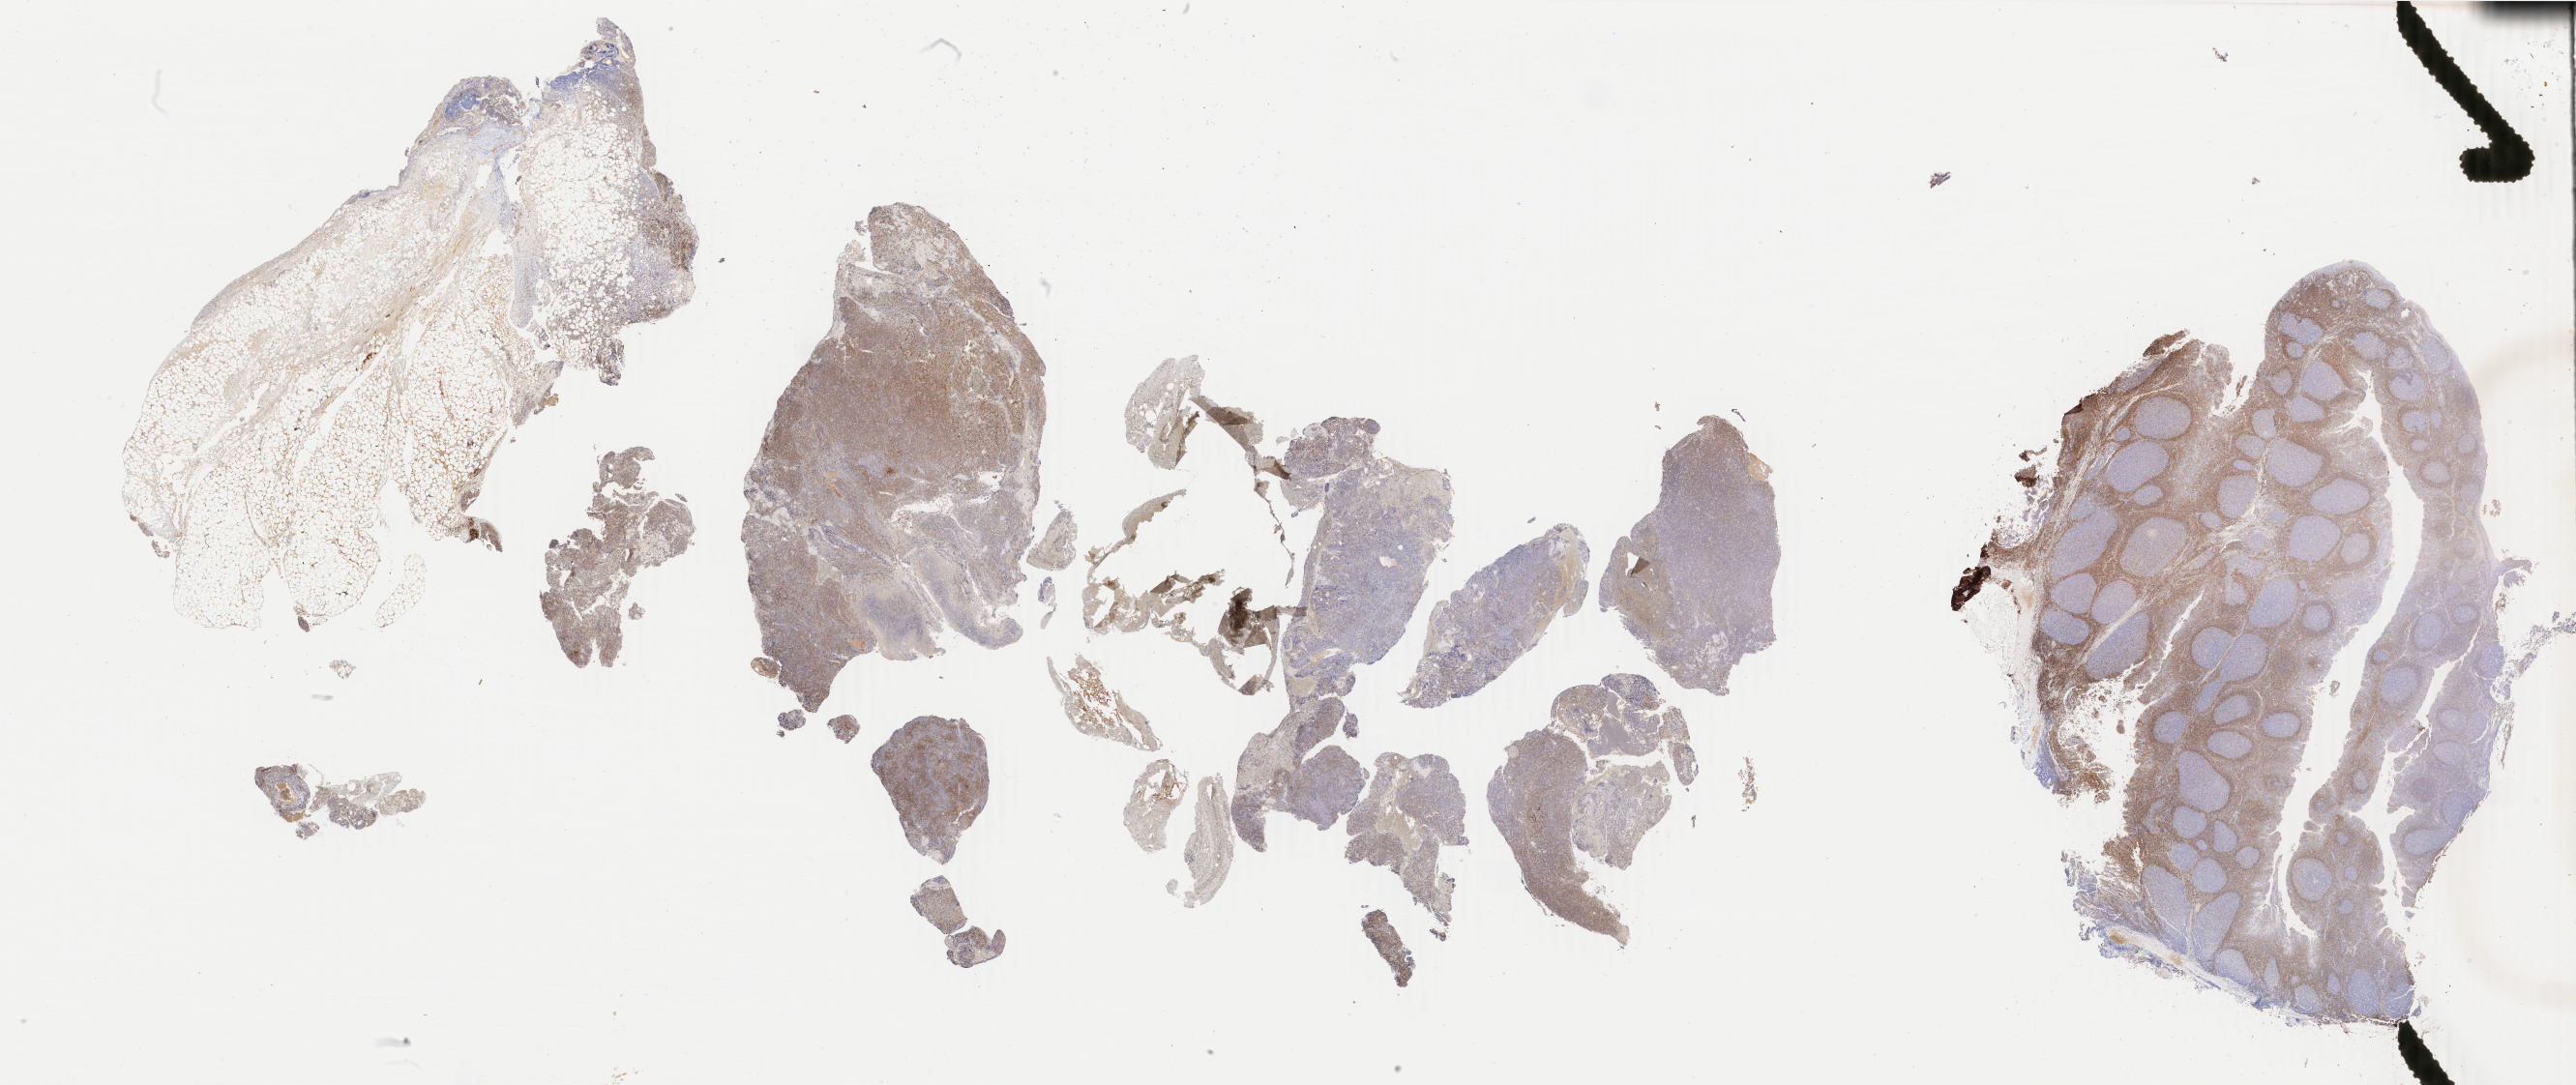
IHC for BCL2, whole-slide image — a low-resolution overview of the entire scanned area, about 42.4 x 17.8 mm, specimen: tumor tissue, site: abdominal lymph node. Patient: male, 27 years old.
Histologic diagnosis: Burkitt lymphoma, NOS.